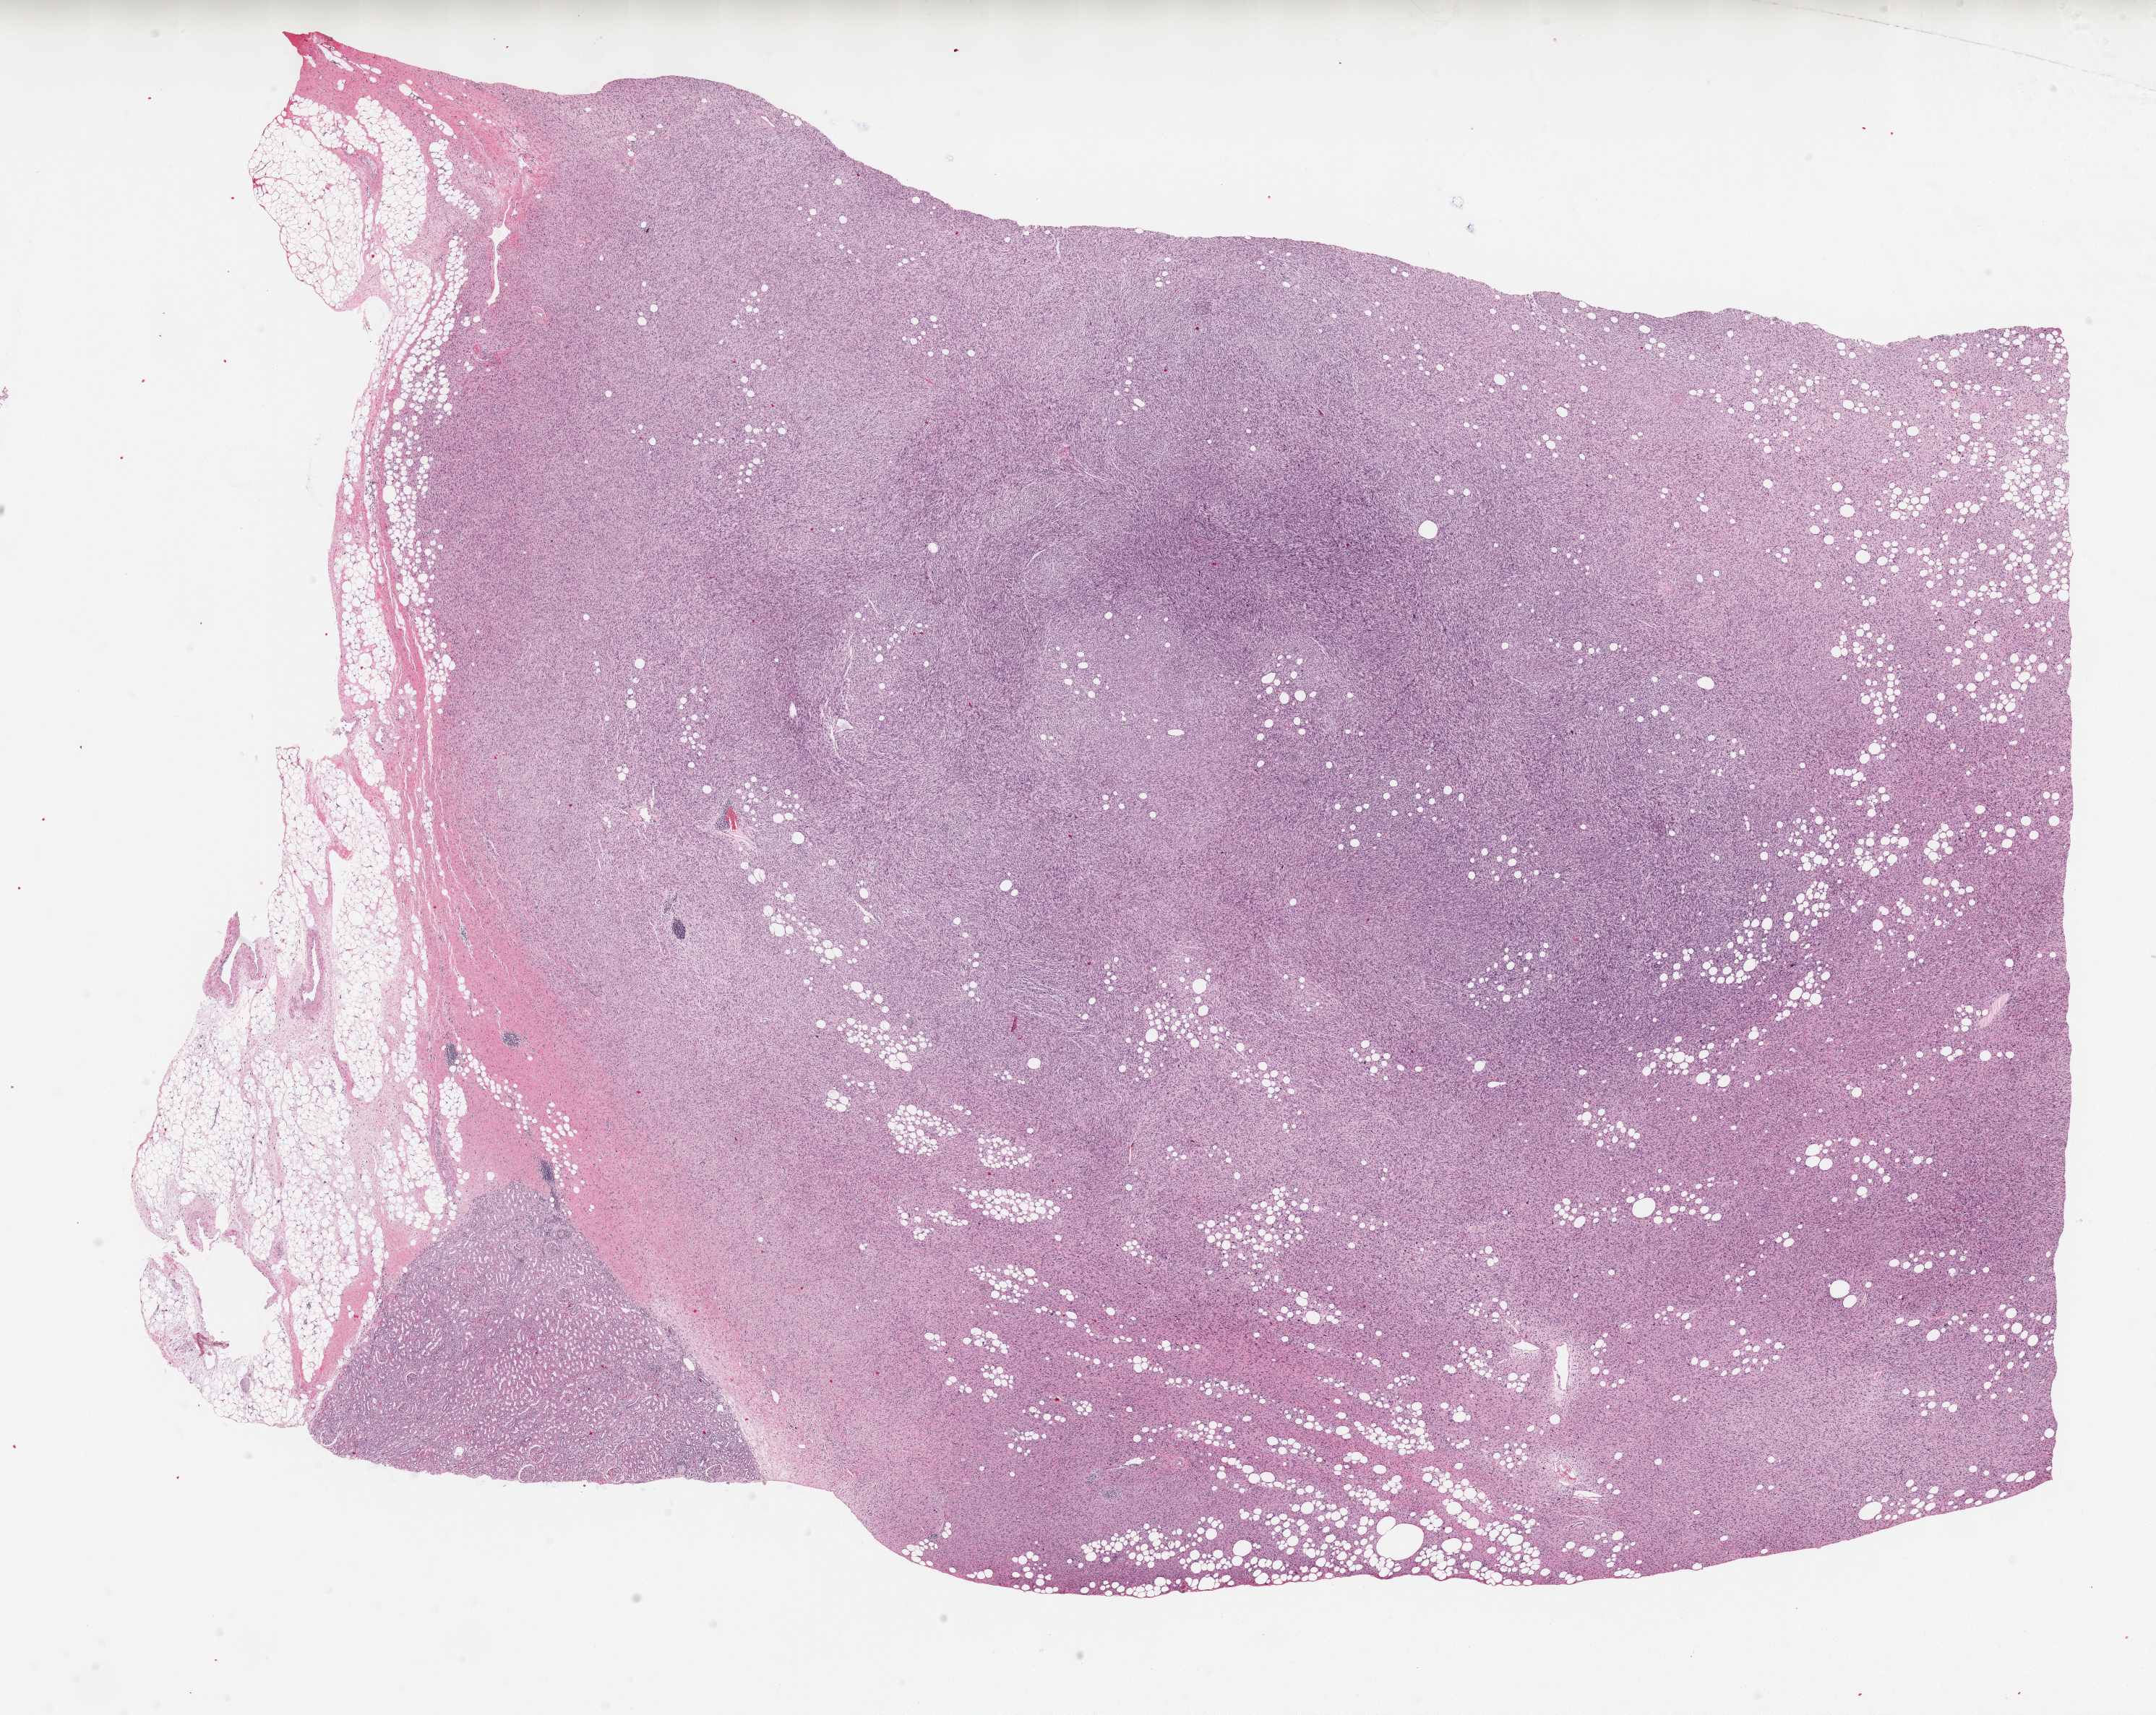
Whole-slide histology image, H&E-stained, whole scanned area (about 23.8 x 18.9 mm) shown as a low-resolution overview, formalin-fixed paraffin-embedded (FFPE) diagnostic section, retroperitoneum and peritoneum, primary tumour sample. Female patient; age at initial diagnosis 82 years.
Diagnosis: Dedifferentiated liposarcoma (retroperitoneum).